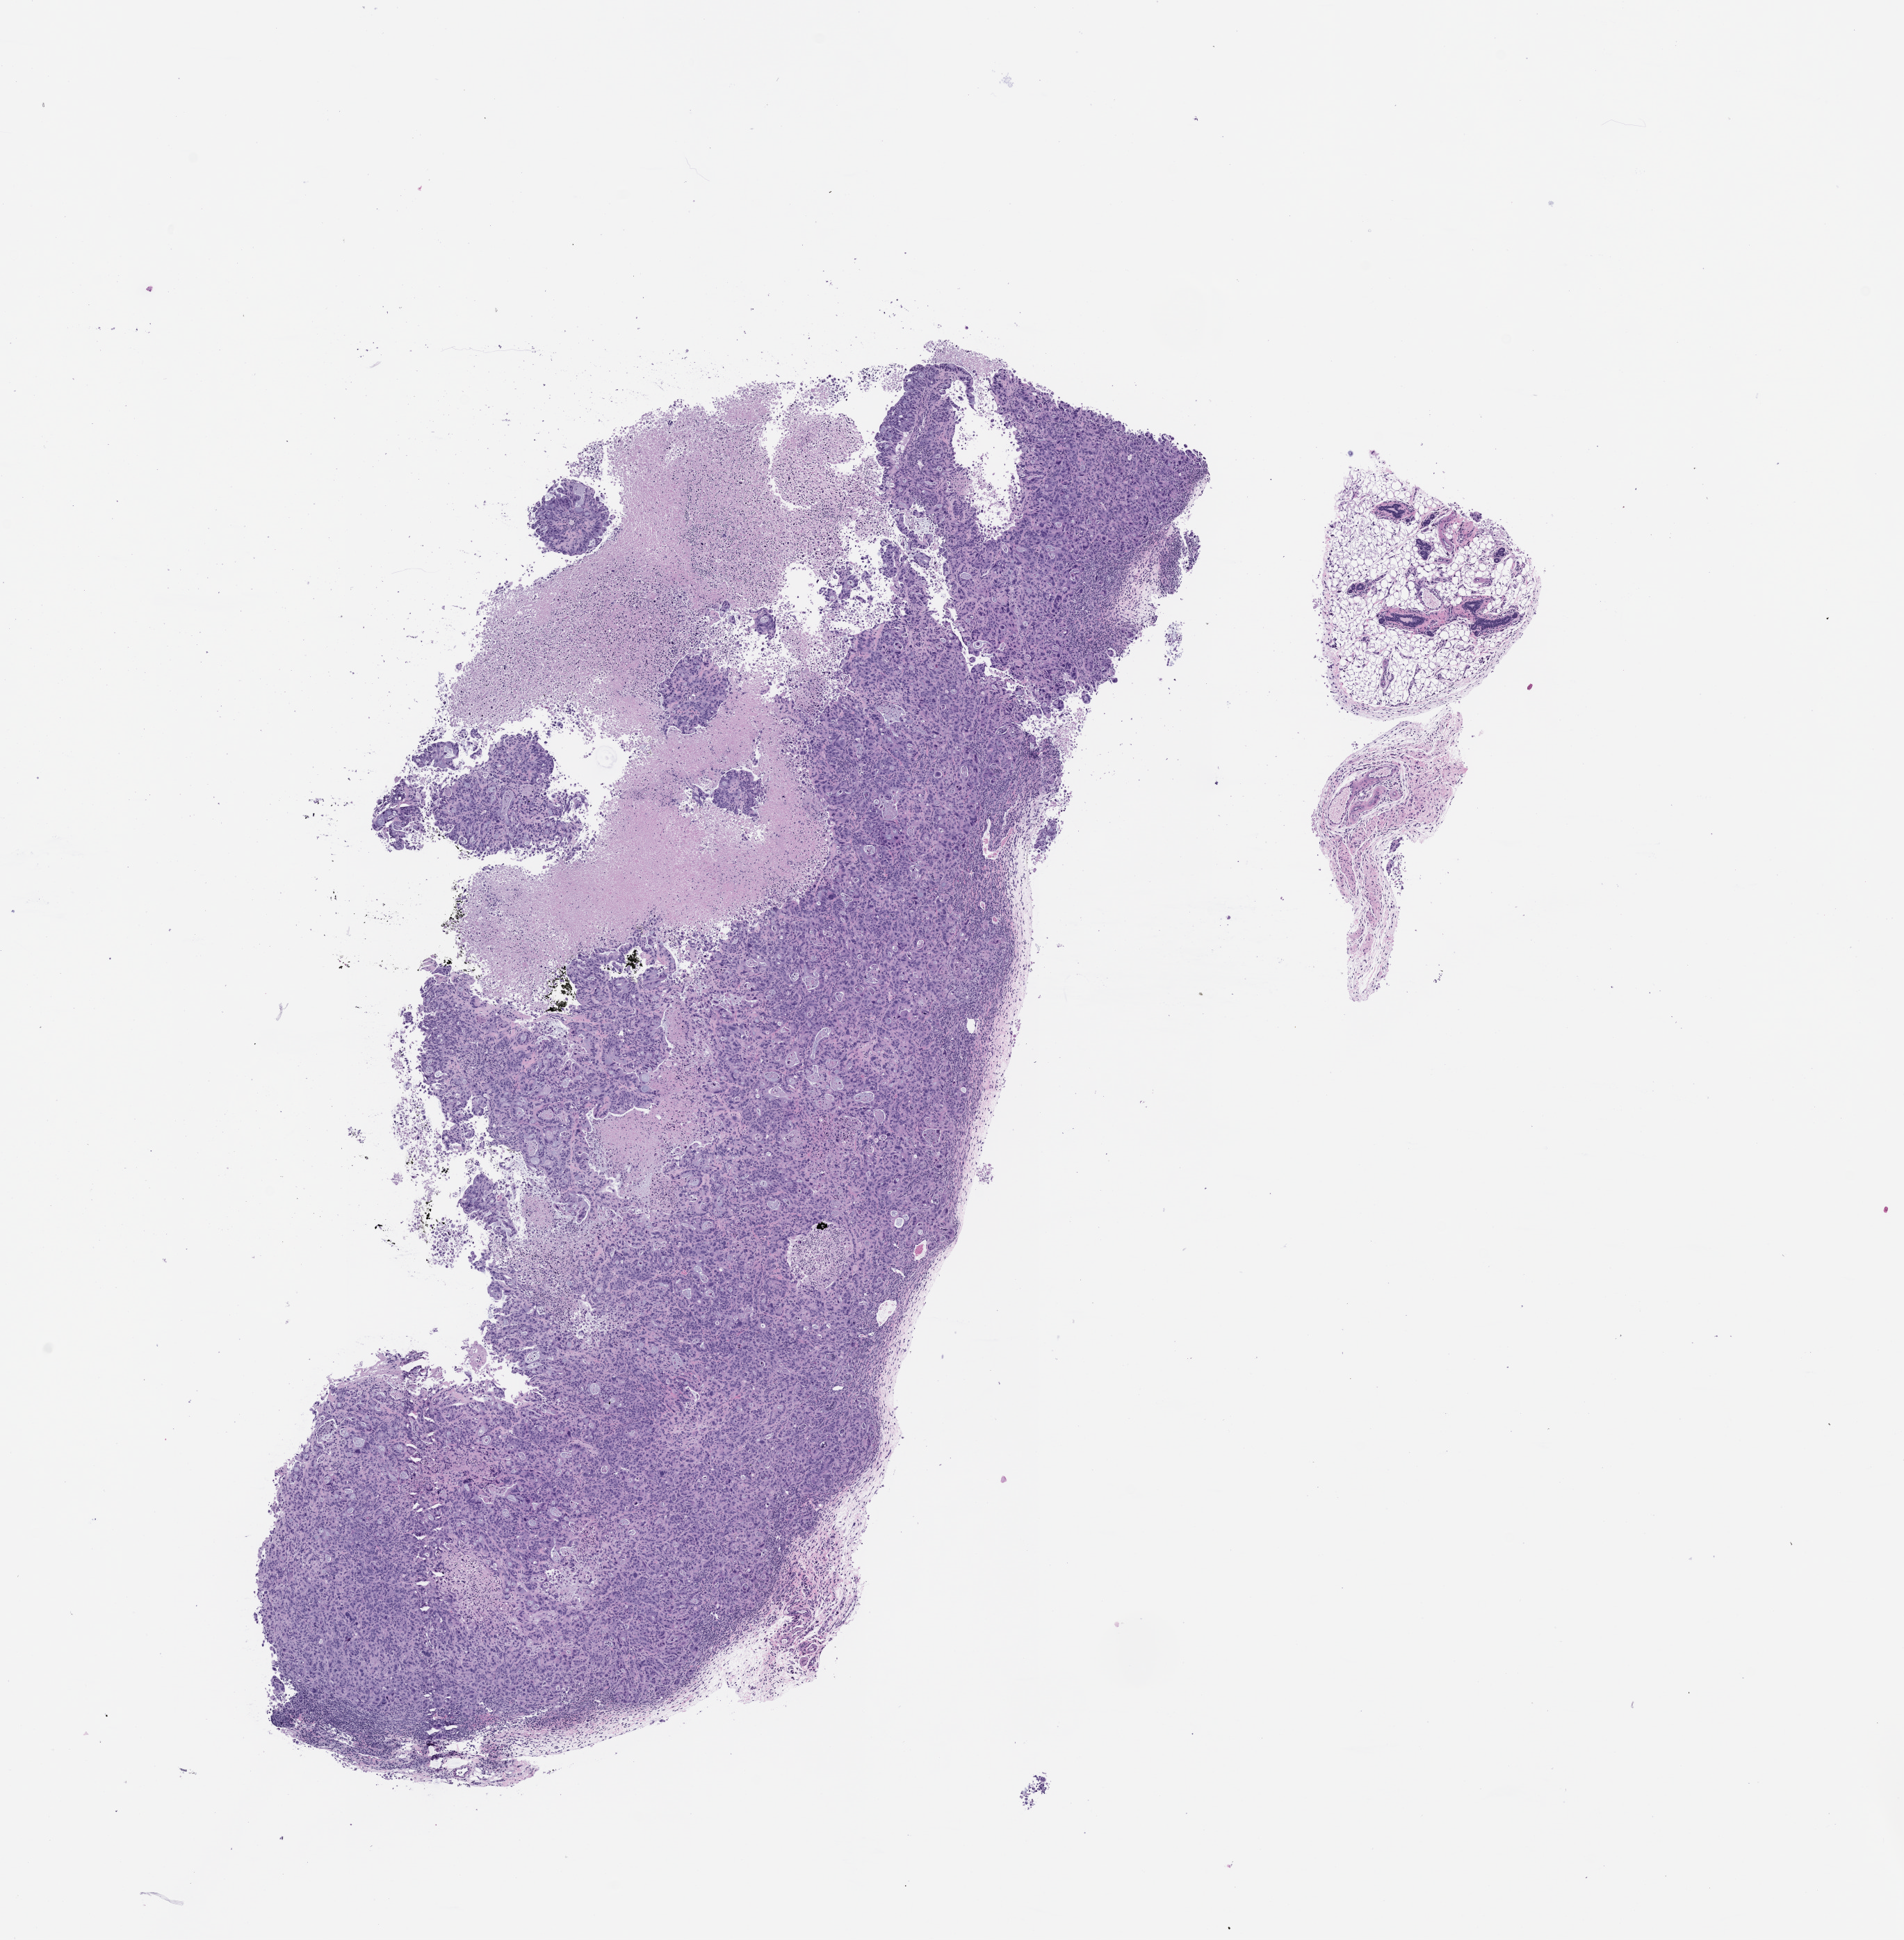
Hematoxylin and eosin (H&E) whole-slide image of a patient-derived xenograft (PDX) tumor grown in a mouse, passage 3, whole scanned area (about 11.0 x 11.2 mm) shown as a low-resolution overview, formalin-fixed, paraffin-embedded (FFPE) tissue, tumor site category: pancreas.
Originating patient diagnosis: Pancreatic Adenocarcinoma.